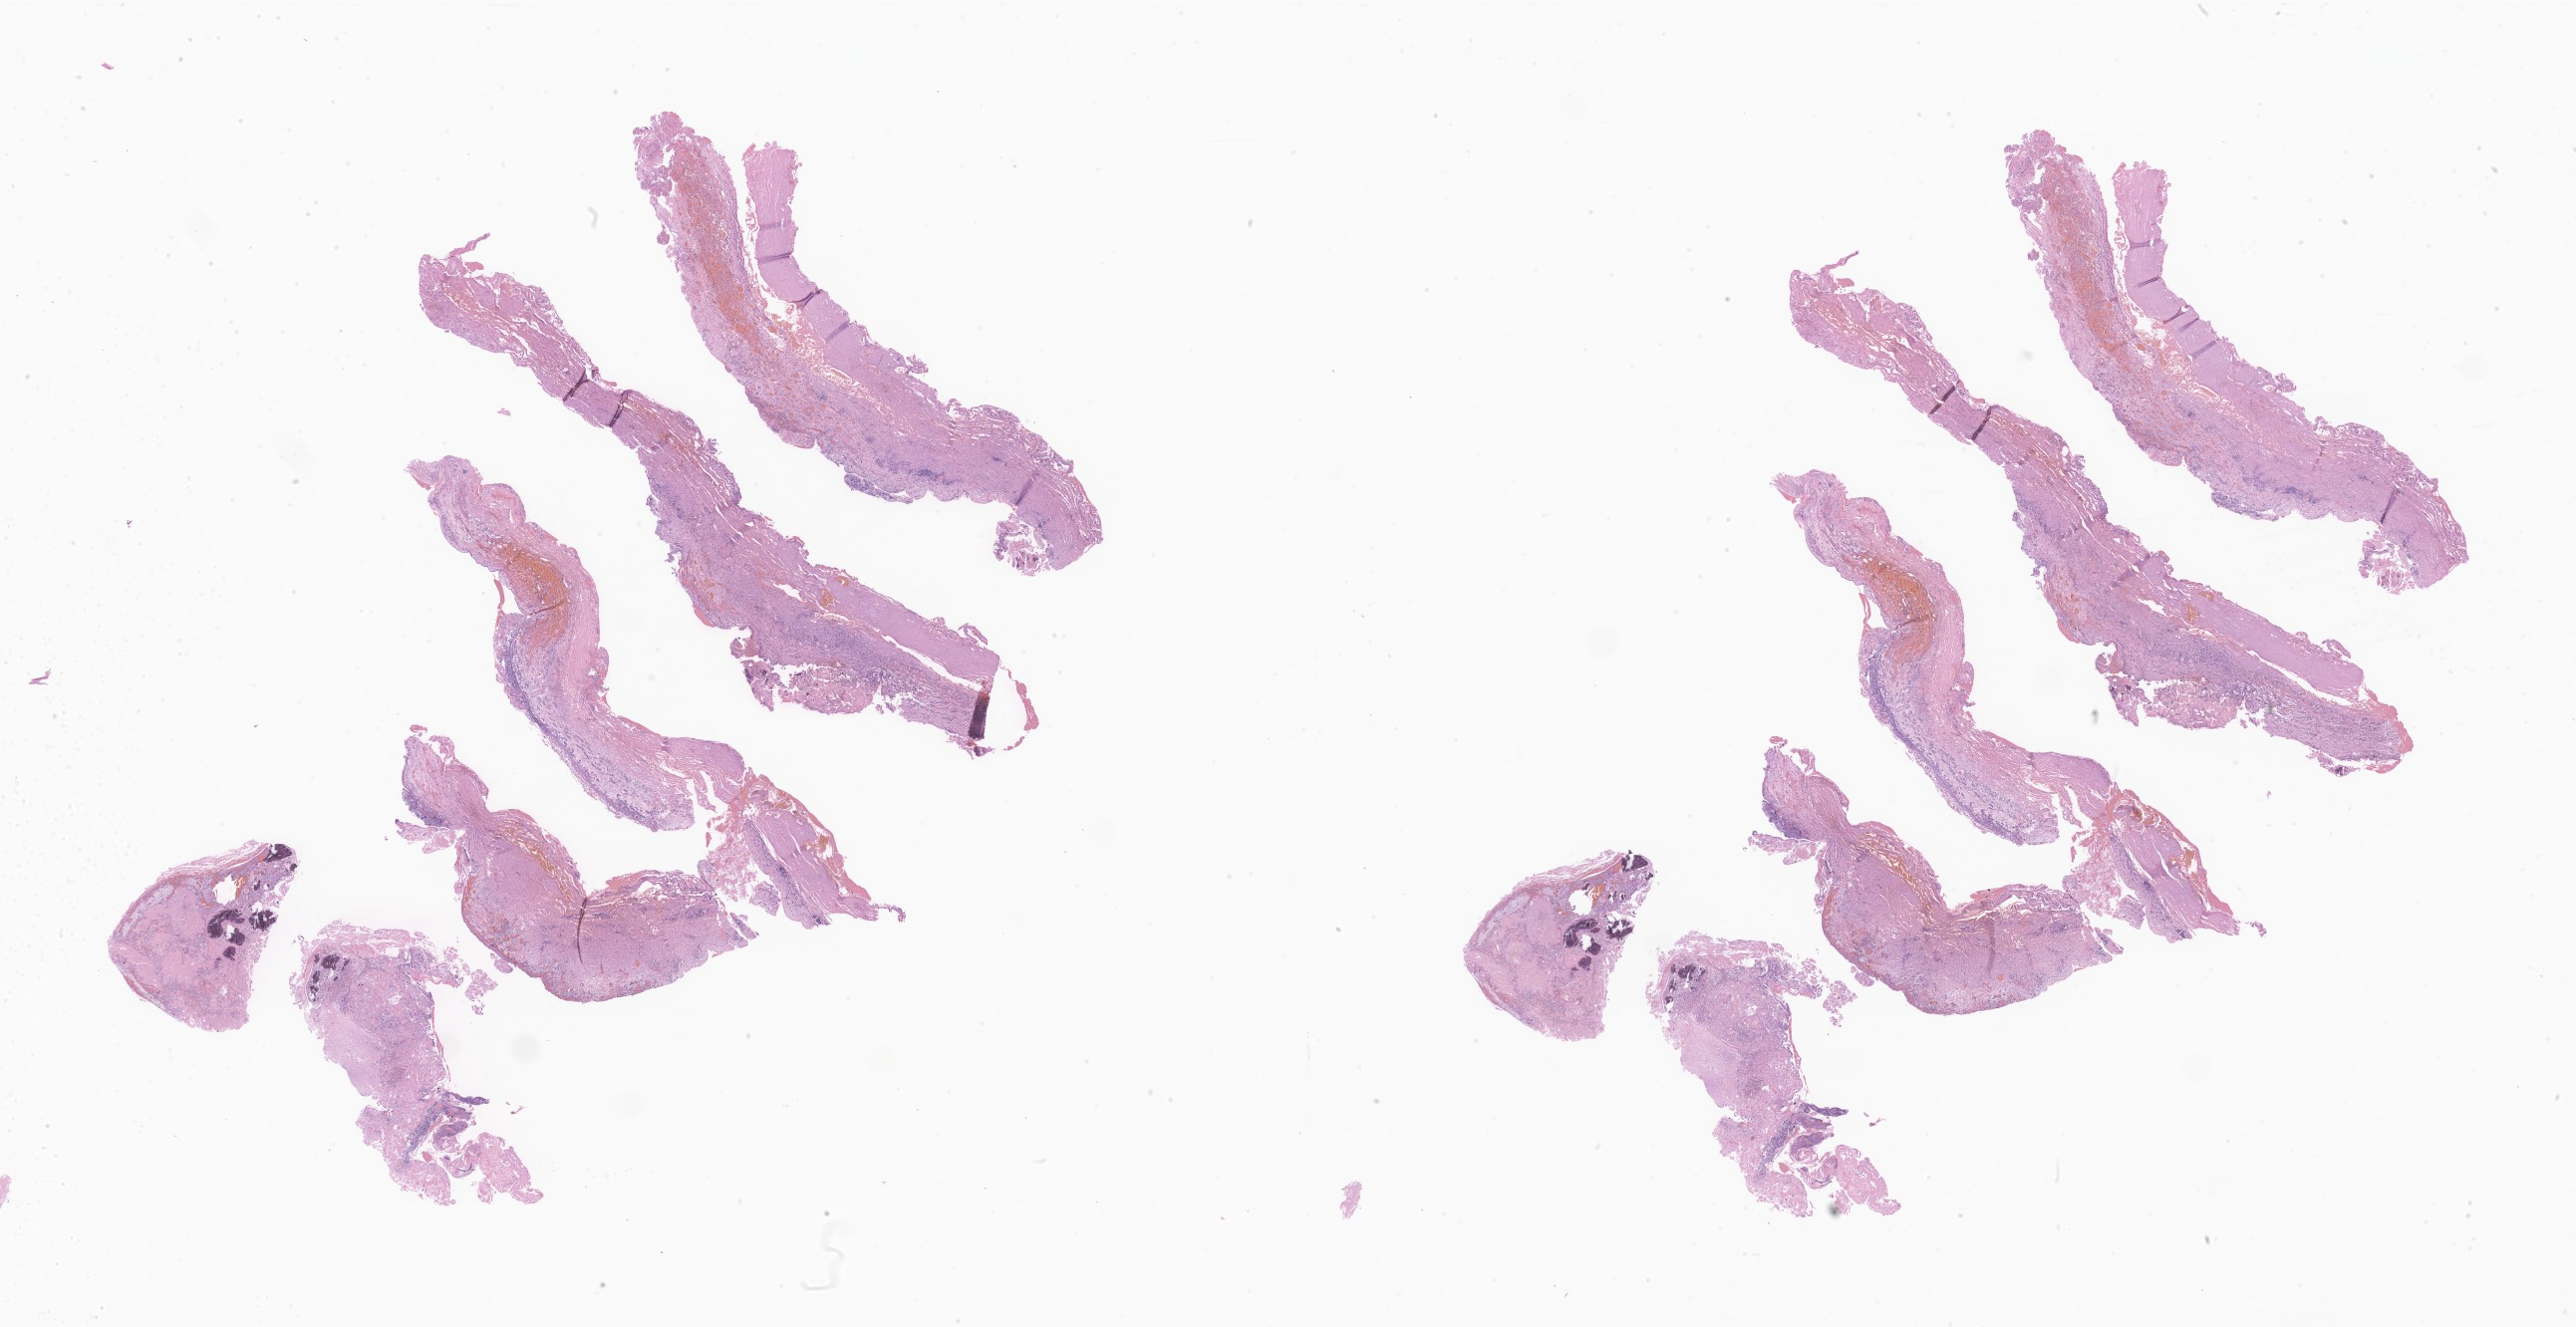
H&E whole-slide image of tumor tissue from the brain — a low-resolution overview of the entire scanned area, about 43.6 x 22.5 mm; formalin-fixed paraffin-embedded section. Patient male; age 133 months (11 years 1 month).
- diagnosis: Craniopharyngioma, adamantinomatous